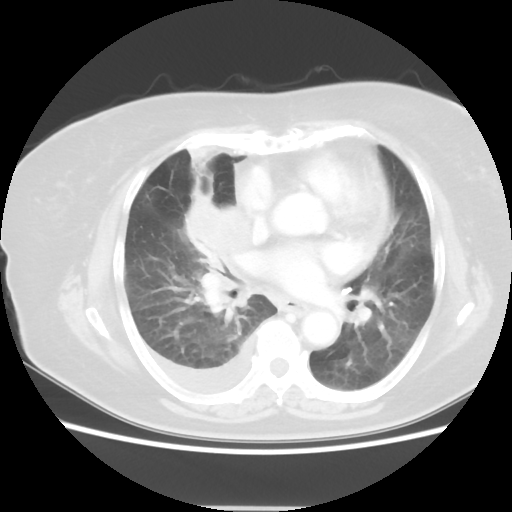
Chest CT, one axial slice; slice 25 of 48 in the series (ordered by position); reconstruction kernel STANDARD; lung window (W 1500 / L -600 HU); 512 × 512 image matrix, field of view 360 × 360 mm. Female patient, age 73 years. Case-level facts recorded for this patient, not image findings: clinical TNM (as recorded): T3 N3 M1b; histopathological grade: G3.
Structures marked on this image (bounding box drawn by a radiologist):
- lung tumour (recorded histology: small cell carcinoma): box from (x=185, y=194) to (x=260, y=325) px